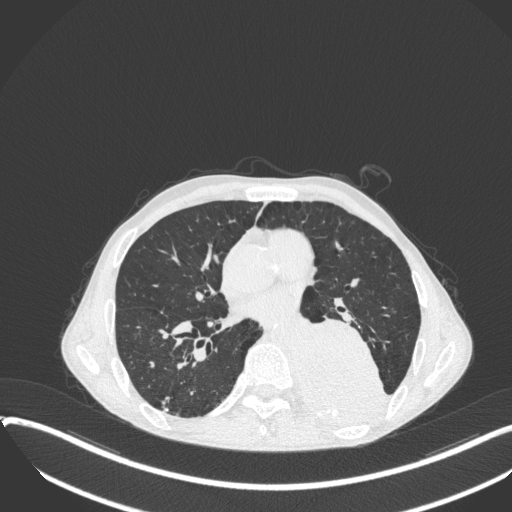
Chest CT, one axial slice; position 180 of 400 along the scan axis; 120 kVp; lung window (W 1500 / L -600 HU); 1 mm slice thickness; 512 × 512 image matrix, field of view 400 × 400 mm. Patient: male, 57 years. From the clinical record (not read from this slice): clinical TNM (as recorded): T4 N0 M0.
Structures marked on this image (rectangle marked by the reading radiologist):
- lung tumour (recorded histology: squamous cell carcinoma): bounding box (x1, y1, x2, y2) in pixels: (303, 315, 390, 425)